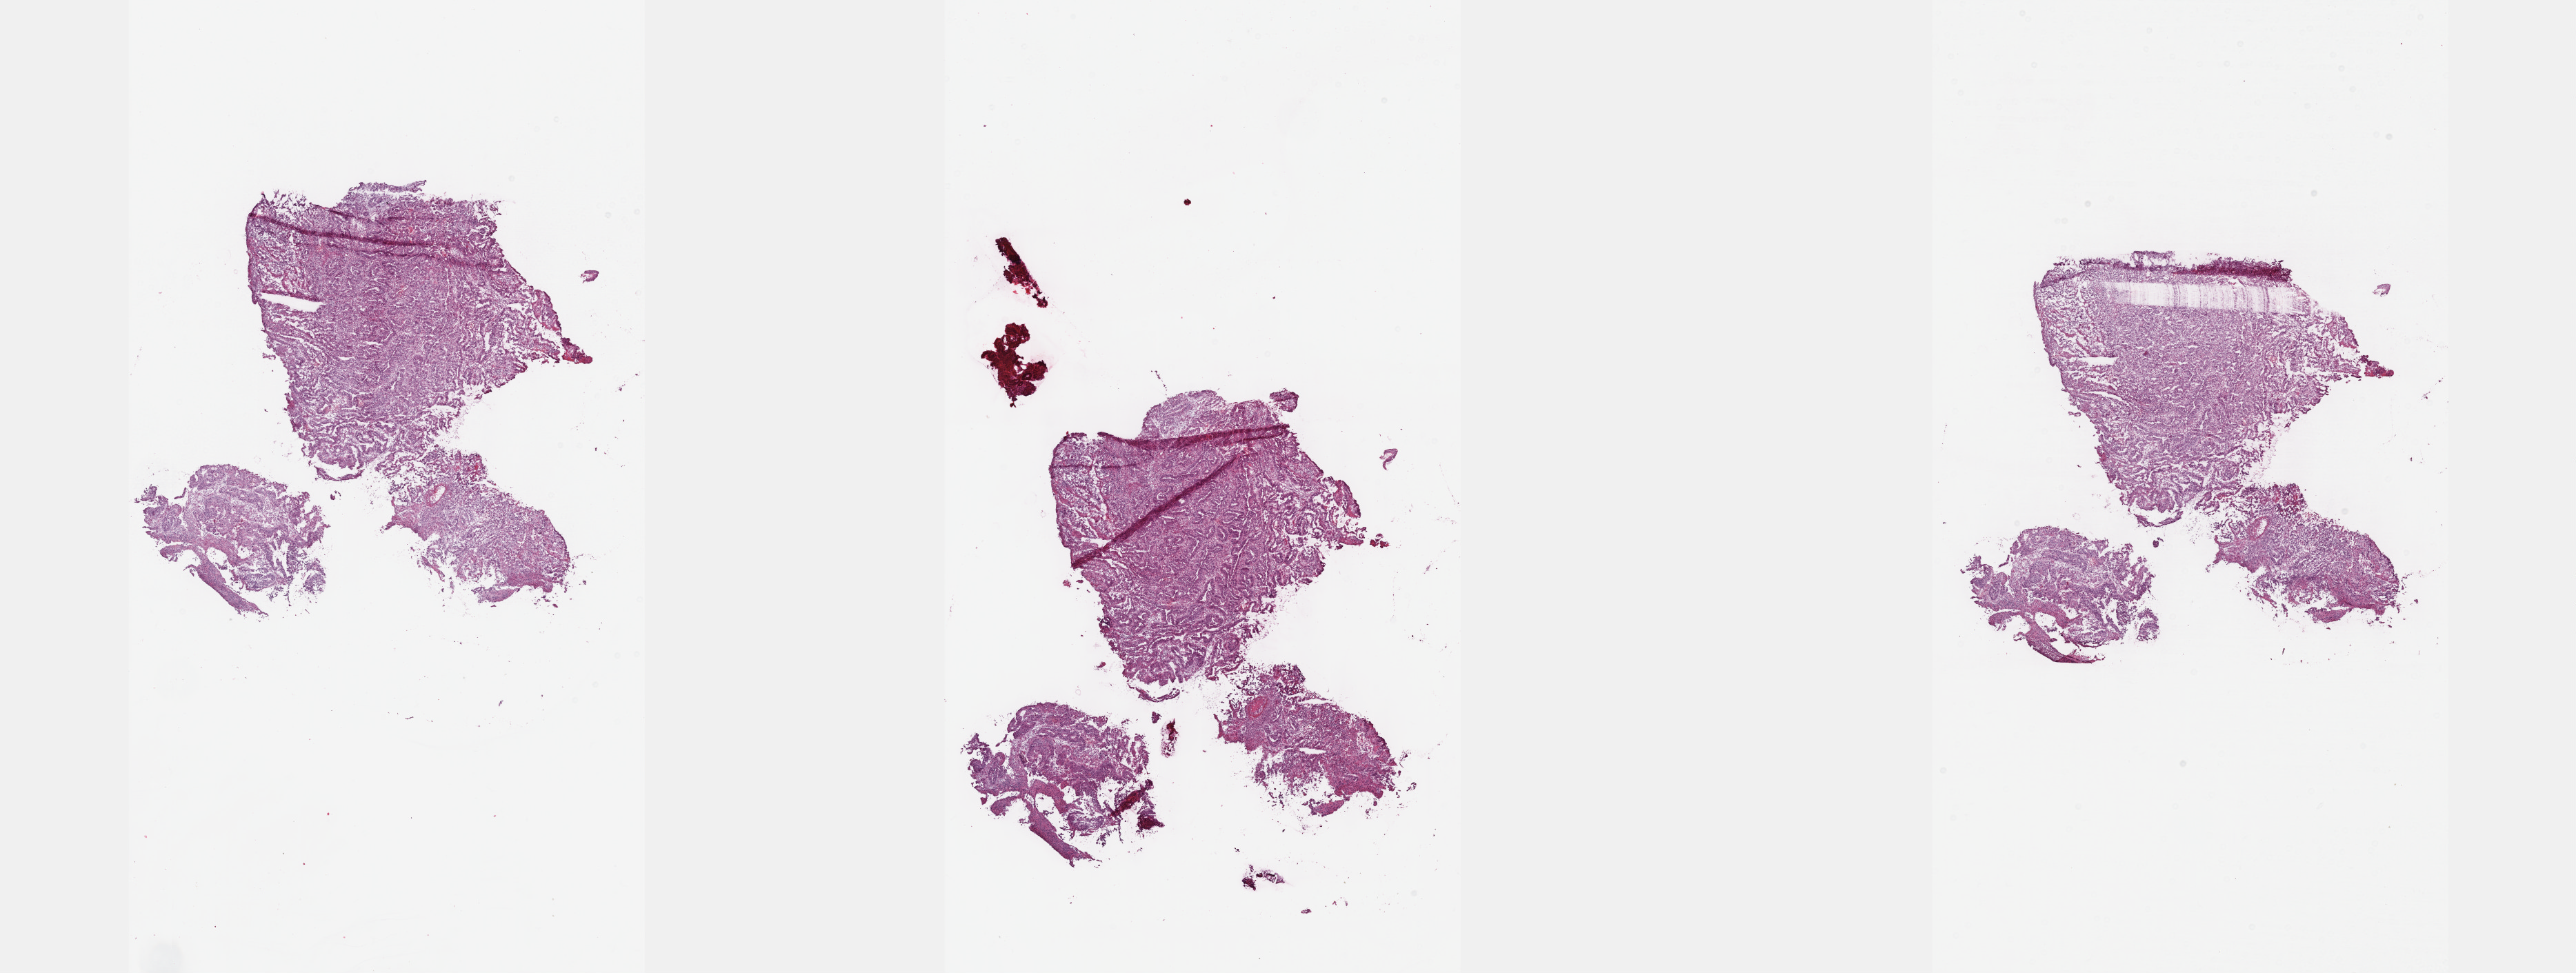
Whole-slide histology image, H&E, shown as a low-resolution overview of the whole scanned area (about 30.2 x 11.4 mm); frozen section from the top of the tissue portion; primary tumour sample from the colon. Female patient; age at initial diagnosis 82 years. Slide review estimates, as recorded: tumour cells 80%, tumour nuclei 60%, normal cells 0%, stromal cells 15%, necrosis 5%. Inflammatory infiltration, as recorded: lymphocyte infiltration 26%, monocyte infiltration 3%, neutrophil infiltration 5%.
Histologic diagnosis: Adenocarcinoma, NOS (cecum). AJCC pathologic stage: IV (6th edition). TNM: T3 N1 M1.